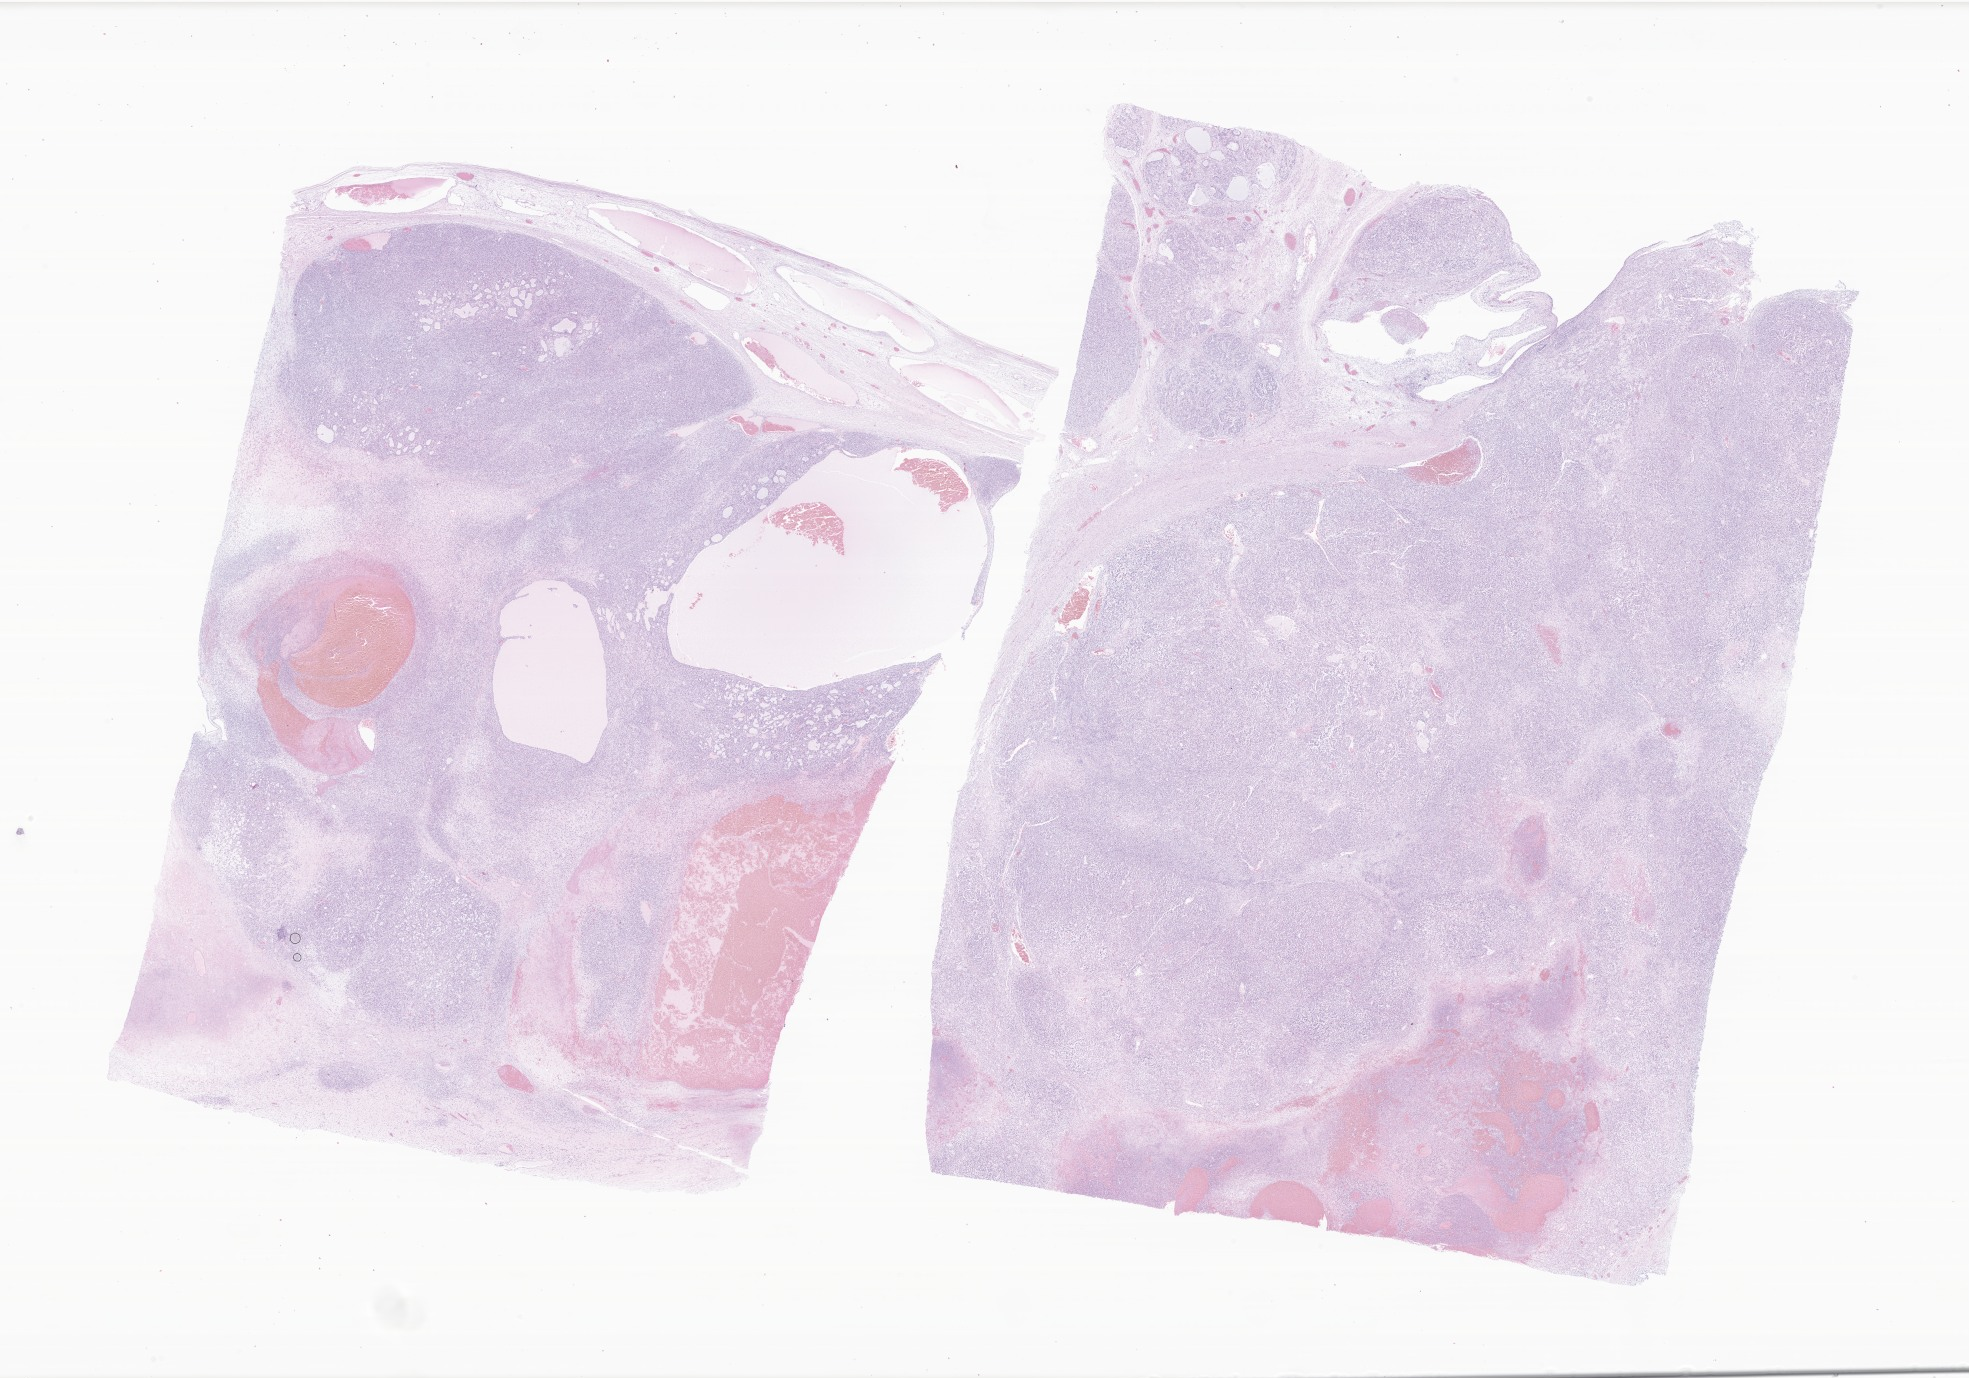
H&E whole-slide image of tumor tissue from the ovary — shown as a low-resolution overview of the whole scanned area (about 33.2 x 23.2 mm). FFPE section. Patient female; age 184 months (15 years 4 months).
• diagnosis: Sertoli-Leydig cell tumor, poorly differentiated